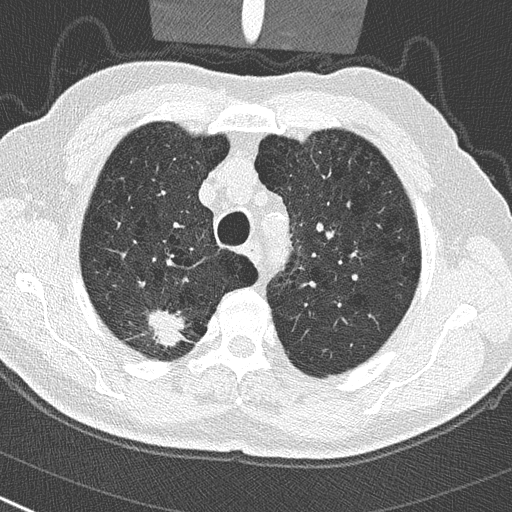
Low-dose screening chest CT, axial slice; first (baseline) screen; lung window (W 1500 / L -600 HU); 2 mm slice thickness; slice 62 of 290 in the series. Male participant, aged 65 years at enrolment. Current smoker at enrolment.
- Expert reader's lesion annotation, bounding box (x1, y1, x2, y2) in pixels: (132, 301, 191, 356).
- Reader record for this screening exam (exam-level; its link to the box is not recorded): non-calcified nodule or mass ≥4 mm, right upper lobe, 24 × 19 mm, spiculated (stellate) margins, soft tissue attenuation.
- Later outcome: lung cancer diagnosed 32 days after this screen — non-small cell carcinoma, right upper lobe, poorly differentiated (G3), stage IA (AJCC 6th edition), 29 mm at pathology.